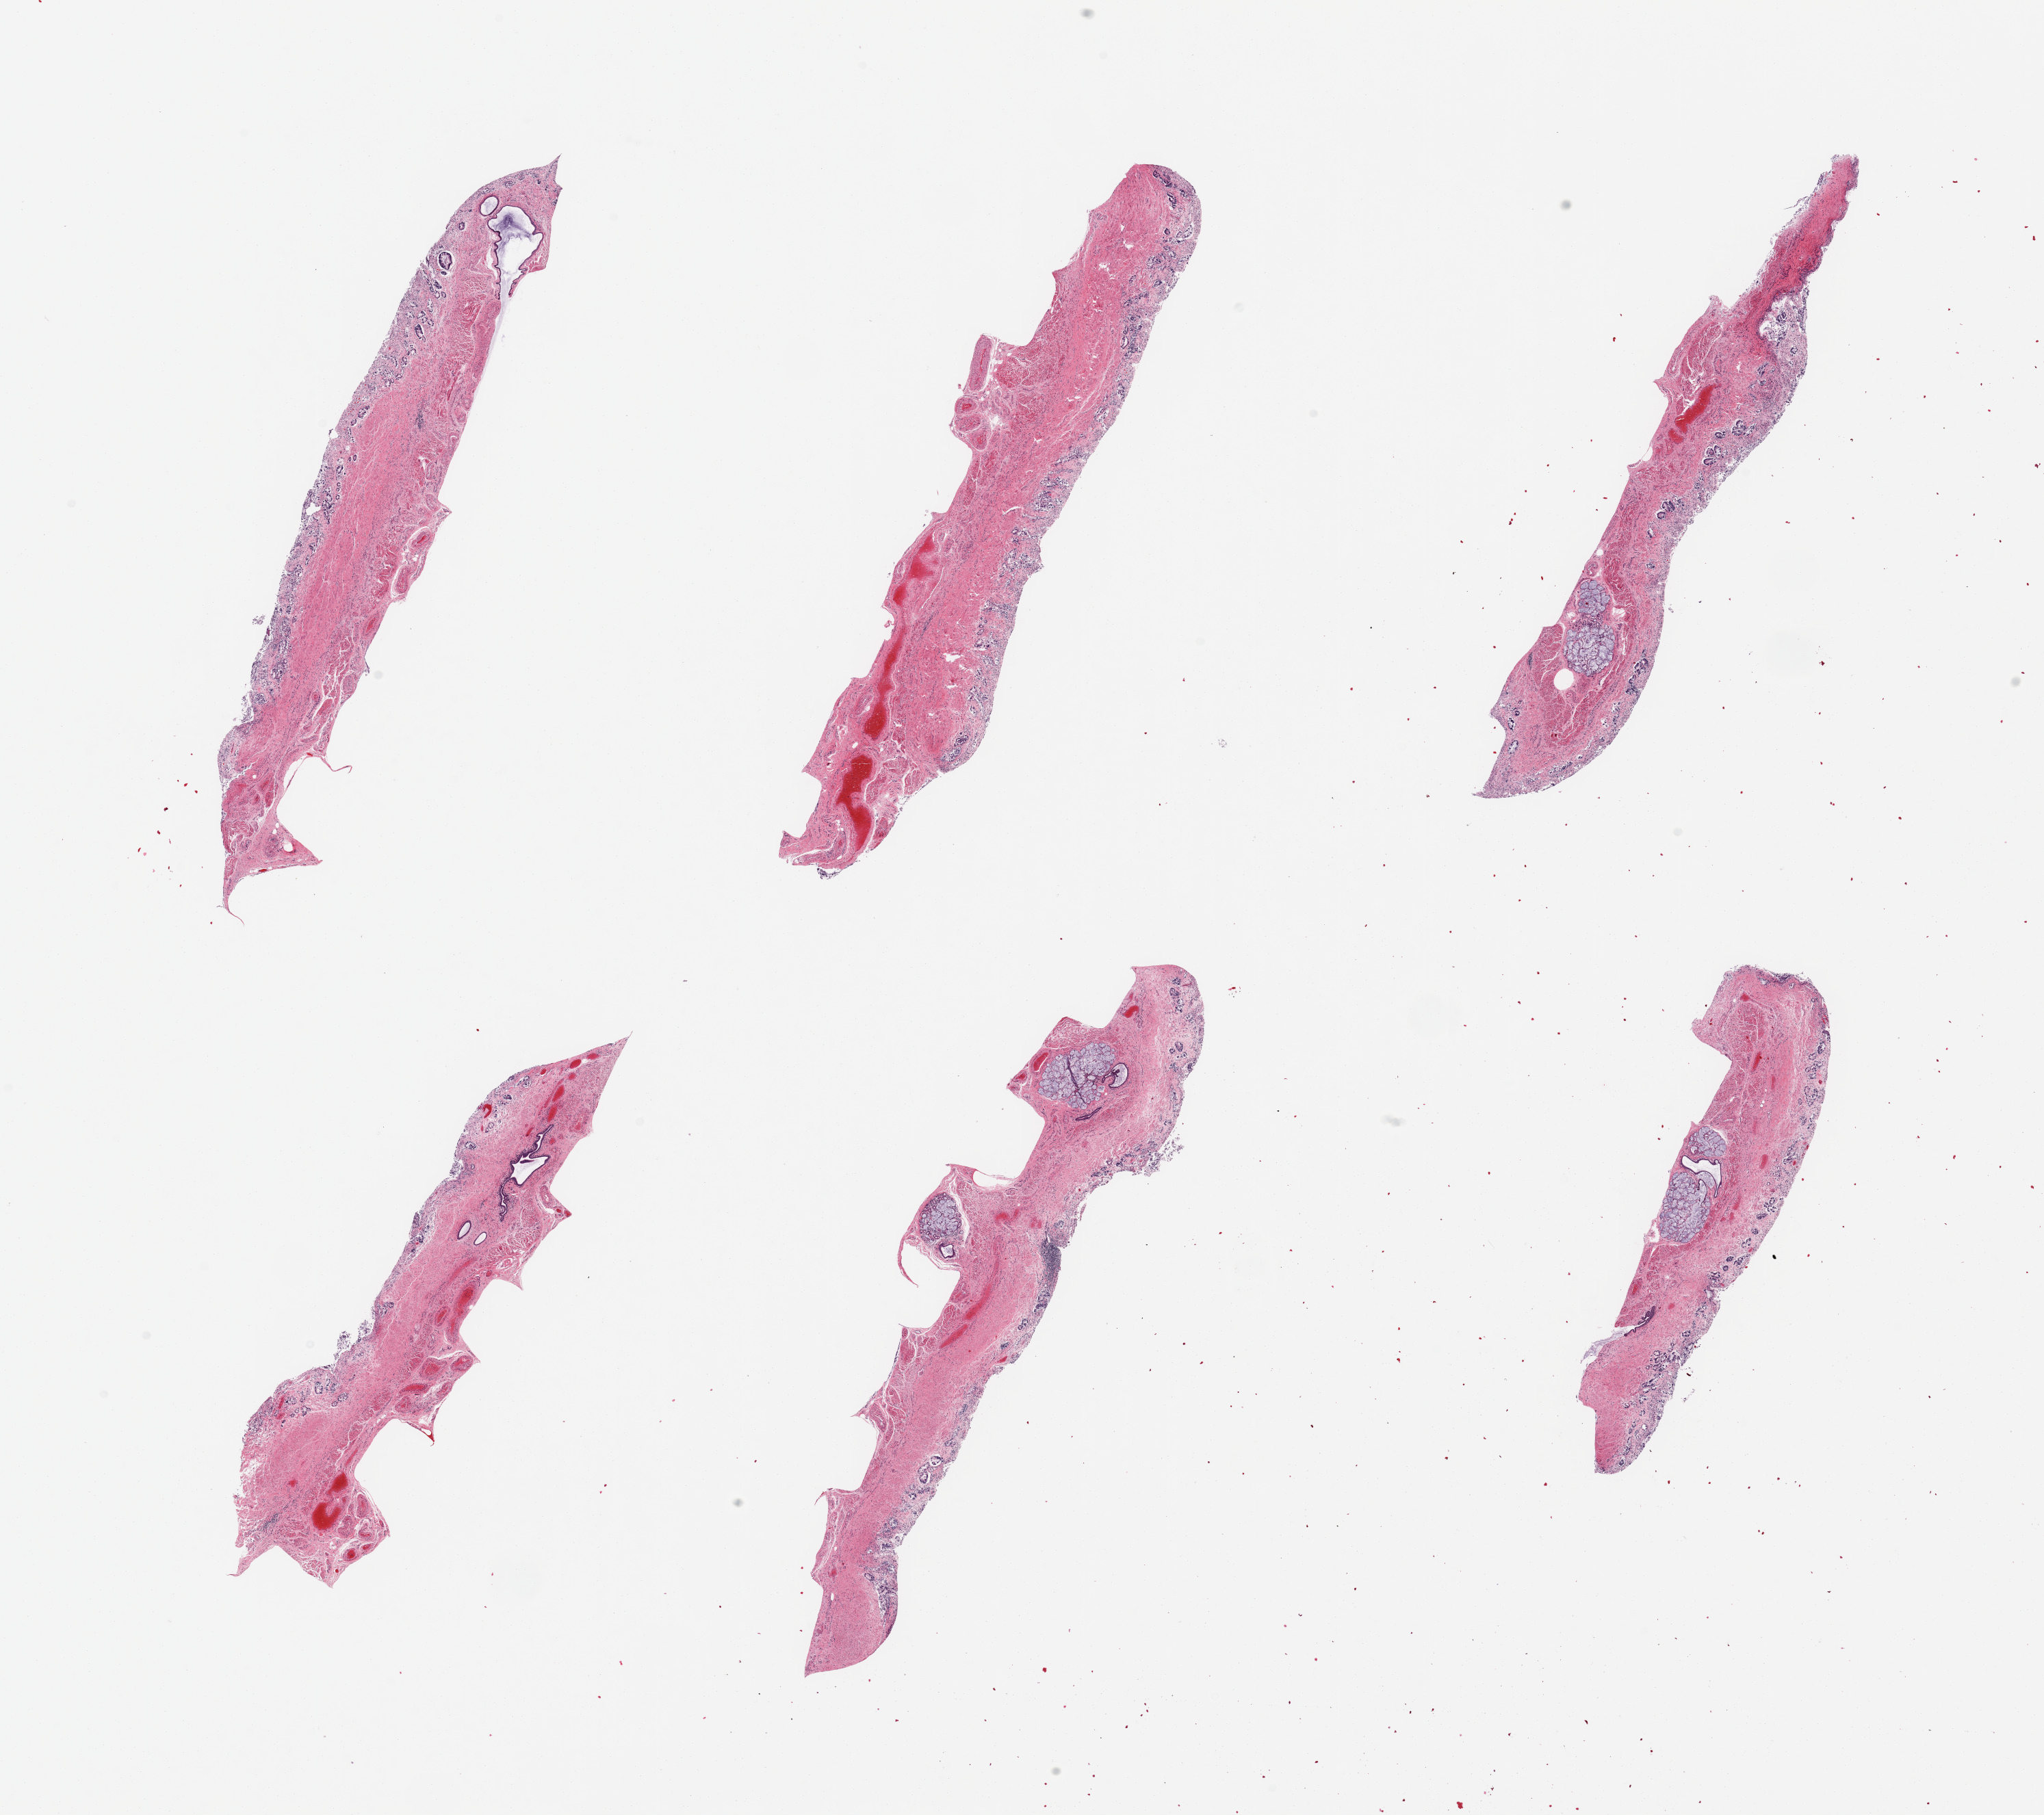
Haematoxylin and eosin whole-slide image, brightfield — a low-resolution overview of the entire scanned area, about 23.6 x 21.0 mm (slide scanned at 20x), PAXgene-fixed, paraffin-embedded tissue, section of esophageal mucous membrane (target tissue), donor tissue sample. Donor sex: male.
Review note (as recorded): 6 pieces; autolyzed glandular mucosa.